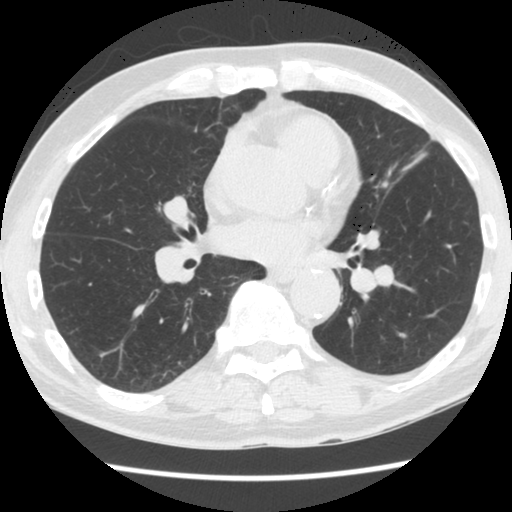
Low-dose screening chest CT, one axial slice; position 77 of 174 along the scan axis; reconstruction kernel STANDARD; 120 kVp; lung window (W 1500 / L -600 HU); 2.5 mm slice thickness; 512 × 512 image matrix, field of view 320 × 320 mm.
Structures marked on this image (expert manual segmentation):
- lesion 1 (tumor, lower lobe of left lung): bounding box (x1, y1, x2, y2) in pixels: (374, 266, 394, 286)